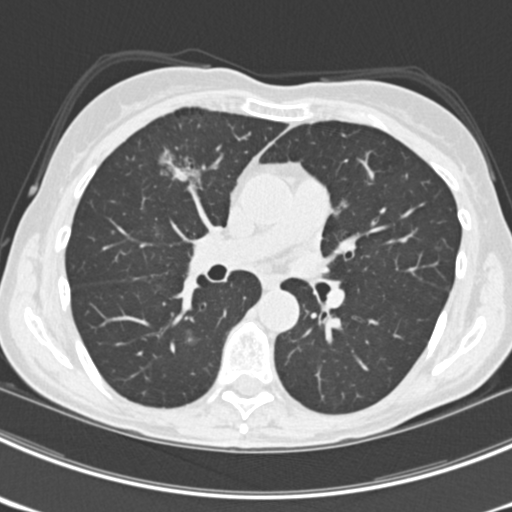
Axial slice from a low-dose chest CT screening exam, third annual screen, lung window (W 1500 / L -600 HU), 2 mm slice thickness, standard (soft-tissue) reconstruction kernel (B30f), 120 kVp, slice 93 of 225 in the series, 512 × 512 image matrix, field of view 302 × 302 mm. Female, age 63 years at enrolment. Current smoker at enrolment.
- Expert reader's lesion annotation, bounding box (x1, y1, x2, y2) in pixels: (152, 139, 218, 198).
- The screening reader recorded 9 non-calcified nodules or masses ≥4 mm on this exam (left upper lobe, right upper lobe, left upper lobe, left lower lobe, right middle lobe, left lower lobe, left lower lobe, right lower lobe, right lower lobe); which of them this box marks is not recorded.